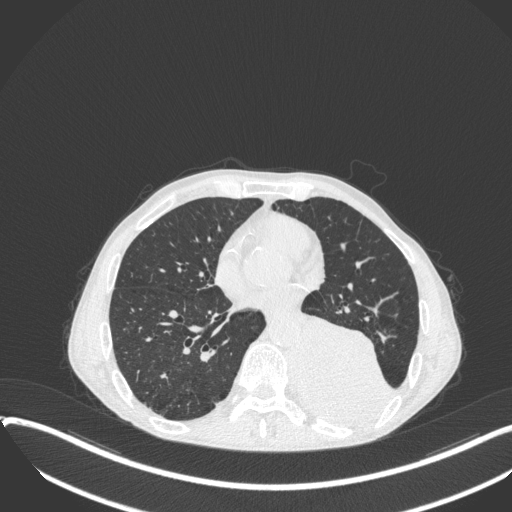
Chest CT, one axial slice. Slice 151 of 400 in the series (ordered by position). Reconstruction kernel B31f. Lung window (W 1500 / L -600 HU). 1 mm slice thickness. 512 × 512 image matrix, field of view 400 × 400 mm. Male patient, age 57 years. From the clinical record (not read from this slice): clinical TNM (as recorded): T4 N0 M0.
Annotated regions visible in this slice (rectangle marked by the reading radiologist):
- lung tumour (recorded histology: squamous cell carcinoma): bounding box [x1, y1, x2, y2] px = [297, 310, 392, 432]